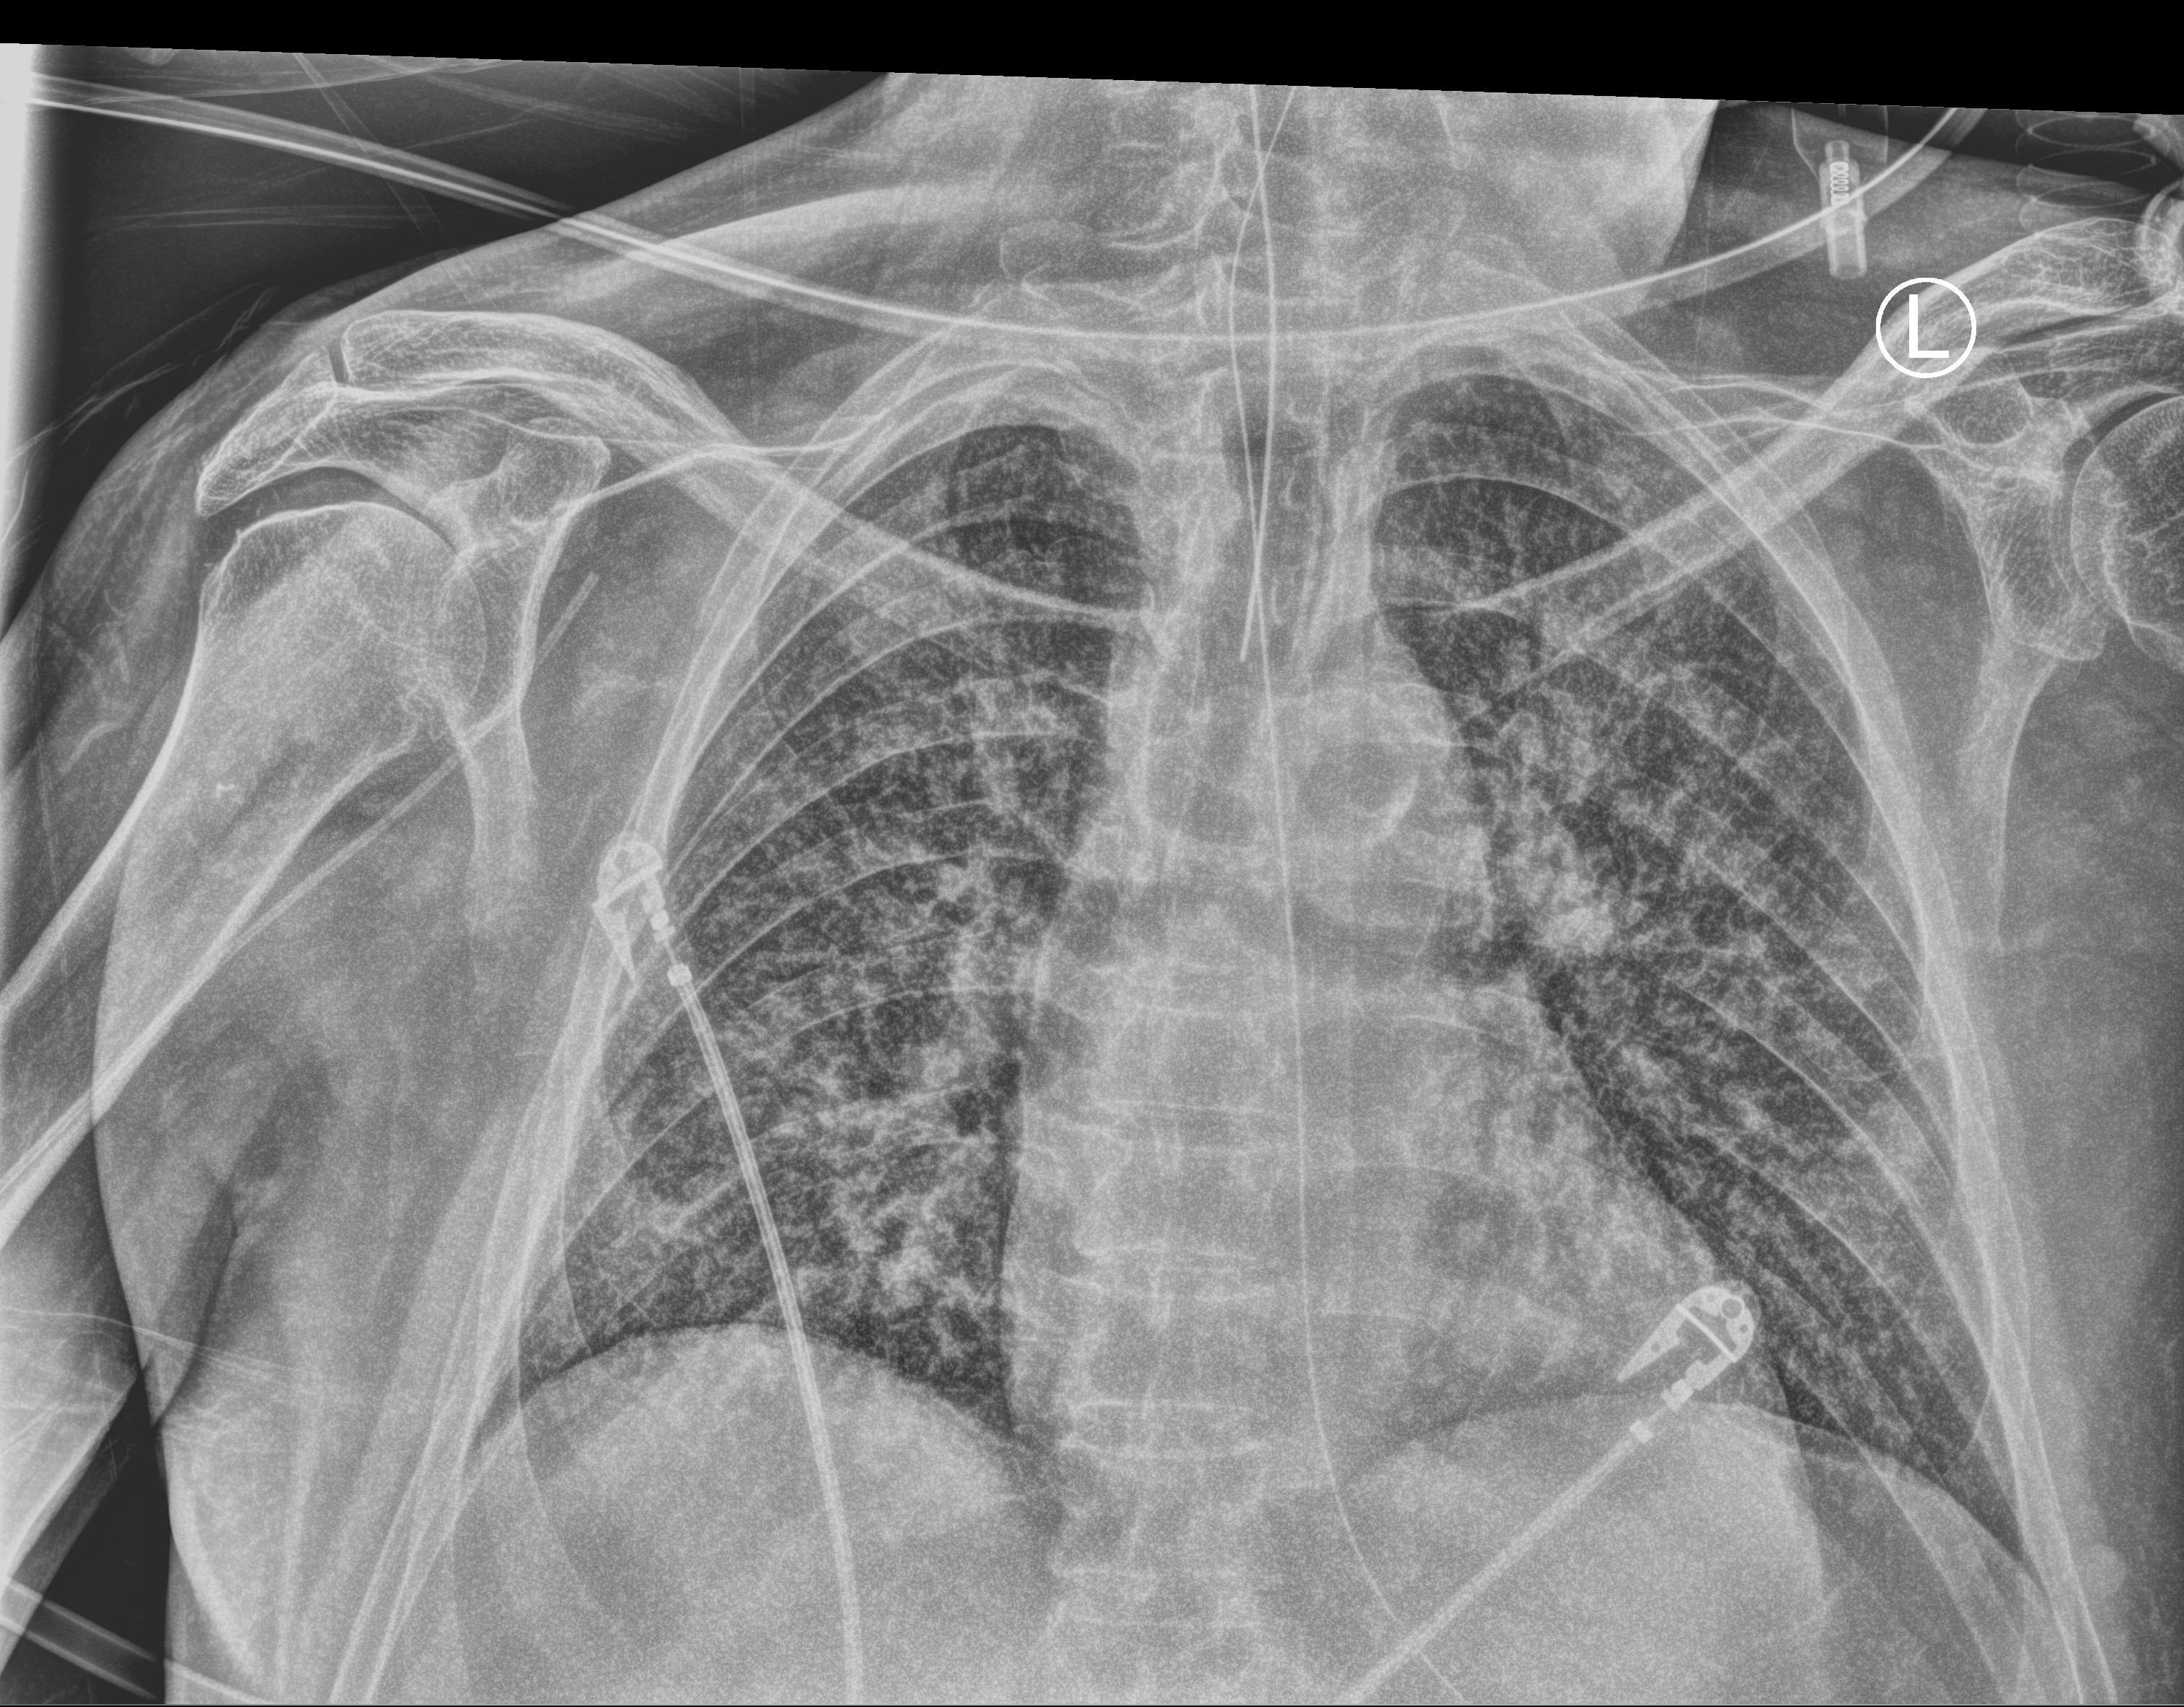
Chest X-ray (portable); anteroposterior (AP) projection. Male patient hospitalised with COVID-19, age 60–74 years.
From the hospital-stay record, not from the radiograph (when in the stay this image was taken is not recorded):
- admitted to intensive care during this hospital stay: yes